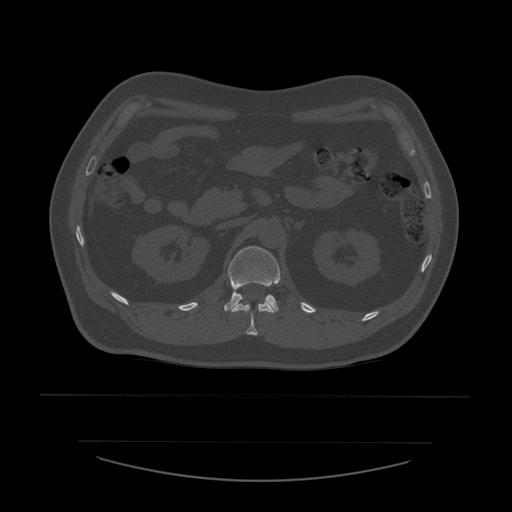
CT including the spine, one axial slice. Slice 236 of 532 in the series (ordered by position). 120 kVp. Bone window (W 1800 / L 400 HU). 512 × 512 image matrix, field of view 441 × 441 mm. Patient age 44 years. From the clinical record (not read from this slice): primary cancer: soft tissue sarcoma.
Outlined on this slice (semi-automatic segmentation, software-assisted and operator-edited):
- L1 vertebra: bounding box [x1, y1, x2, y2] px = [224, 247, 281, 313]
- T12 vertebra: [232, 300, 274, 336]